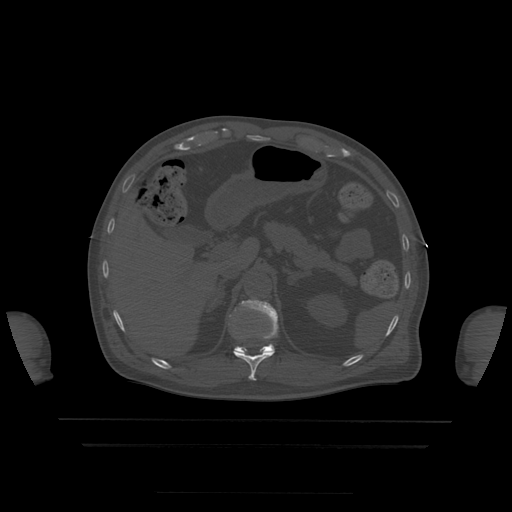
CT including the spine, one axial slice. Position 210 of 522 along the scan axis. Bone window (W 1800 / L 400 HU). 1.25 mm slice thickness. 512 × 512 image matrix, field of view 436 × 436 mm. Patient age 68 years. From the clinical record (not read from this slice): primary cancer: urothelial.
Structures marked on this image (semi-automatically segmented with operator editing):
- T11 vertebra: bounding box [x1, y1, x2, y2] px = [234, 350, 275, 381]
- T12 vertebra: [235, 300, 279, 354]